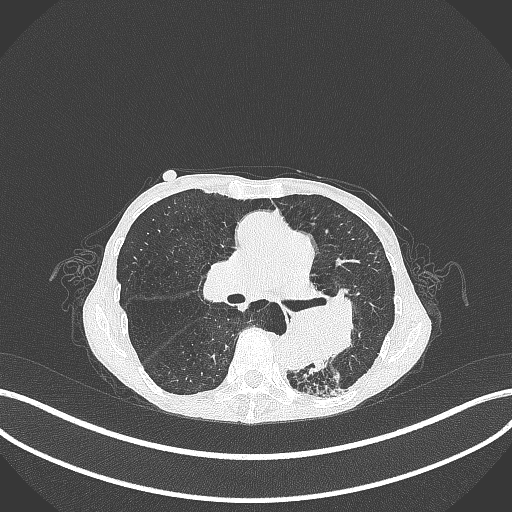
Chest CT, one axial slice. Slice 157 of 347 in the series (ordered by position). 120 kVp. Lung window (W 1500 / L -600 HU). 512 × 512 image matrix, field of view 400 × 400 mm. Patient: female, 70 years. Case-level facts recorded for this patient, not image findings: clinical TNM (as recorded): T3 N0 M0.
Outlined on this slice (rectangle marked by the reading radiologist):
- lung tumour (recorded histology: small cell carcinoma): bounding box [x1, y1, x2, y2] px = [275, 287, 362, 364]